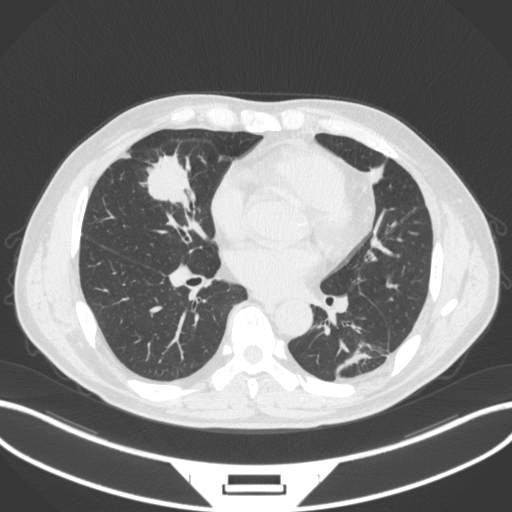
Chest CT, one axial slice; position 132 of 399 along the scan axis; reconstruction kernel B31f; 120 kVp; lung window (W 1500 / L -600 HU); 1 mm slice thickness; 512 × 512 image matrix, field of view 400 × 400 mm. Male patient, age 59 years. From the clinical record (not read from this slice): clinical TNM (as recorded): T2a N1 M0.
Annotated regions visible in this slice (rectangle marked by the reading radiologist):
- lung tumour (recorded histology: adenocarcinoma): bounding box (x1, y1, x2, y2) in pixels: (142, 153, 201, 209)